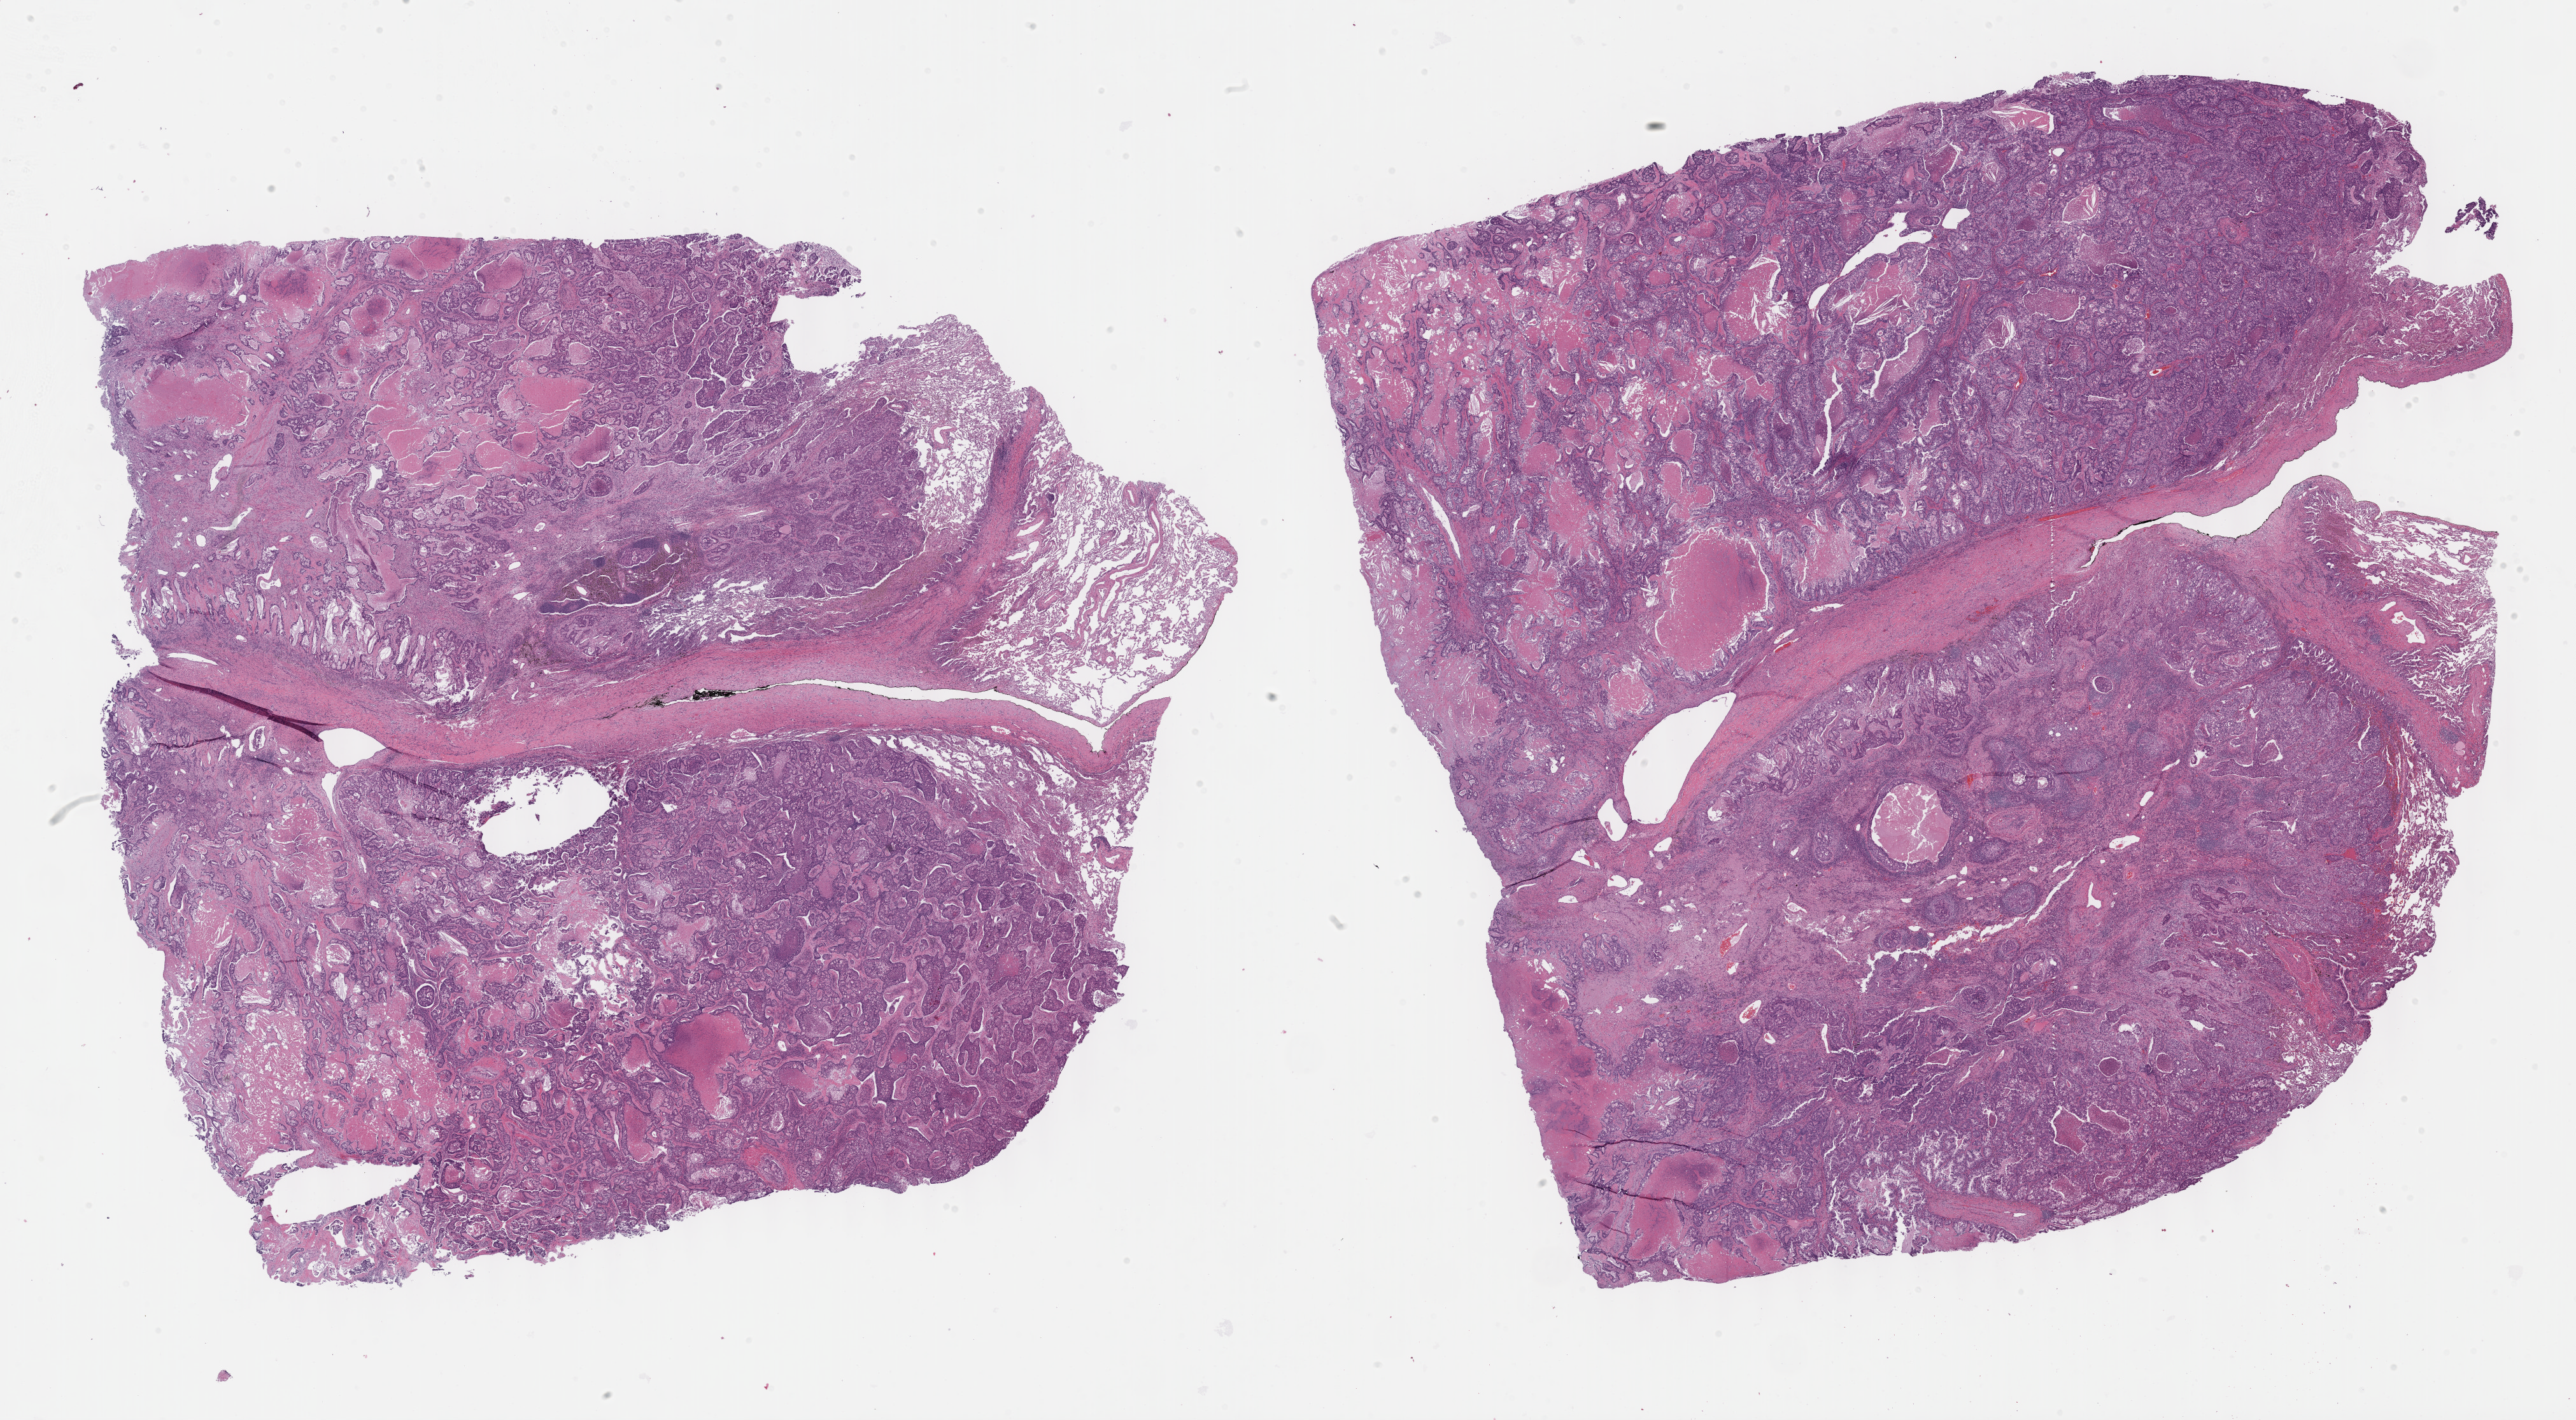
Digitized H&E-stained tissue section (whole slide), whole scanned area (about 32.7 x 18.0 mm, acquisition: 40x scan) shown as a low-resolution overview; FFPE section; primary tumour sample from the lung. Male, age 56 years at initial diagnosis.
Pathologic diagnosis: Adenocarcinoma, NOS (lower lobe, lung).